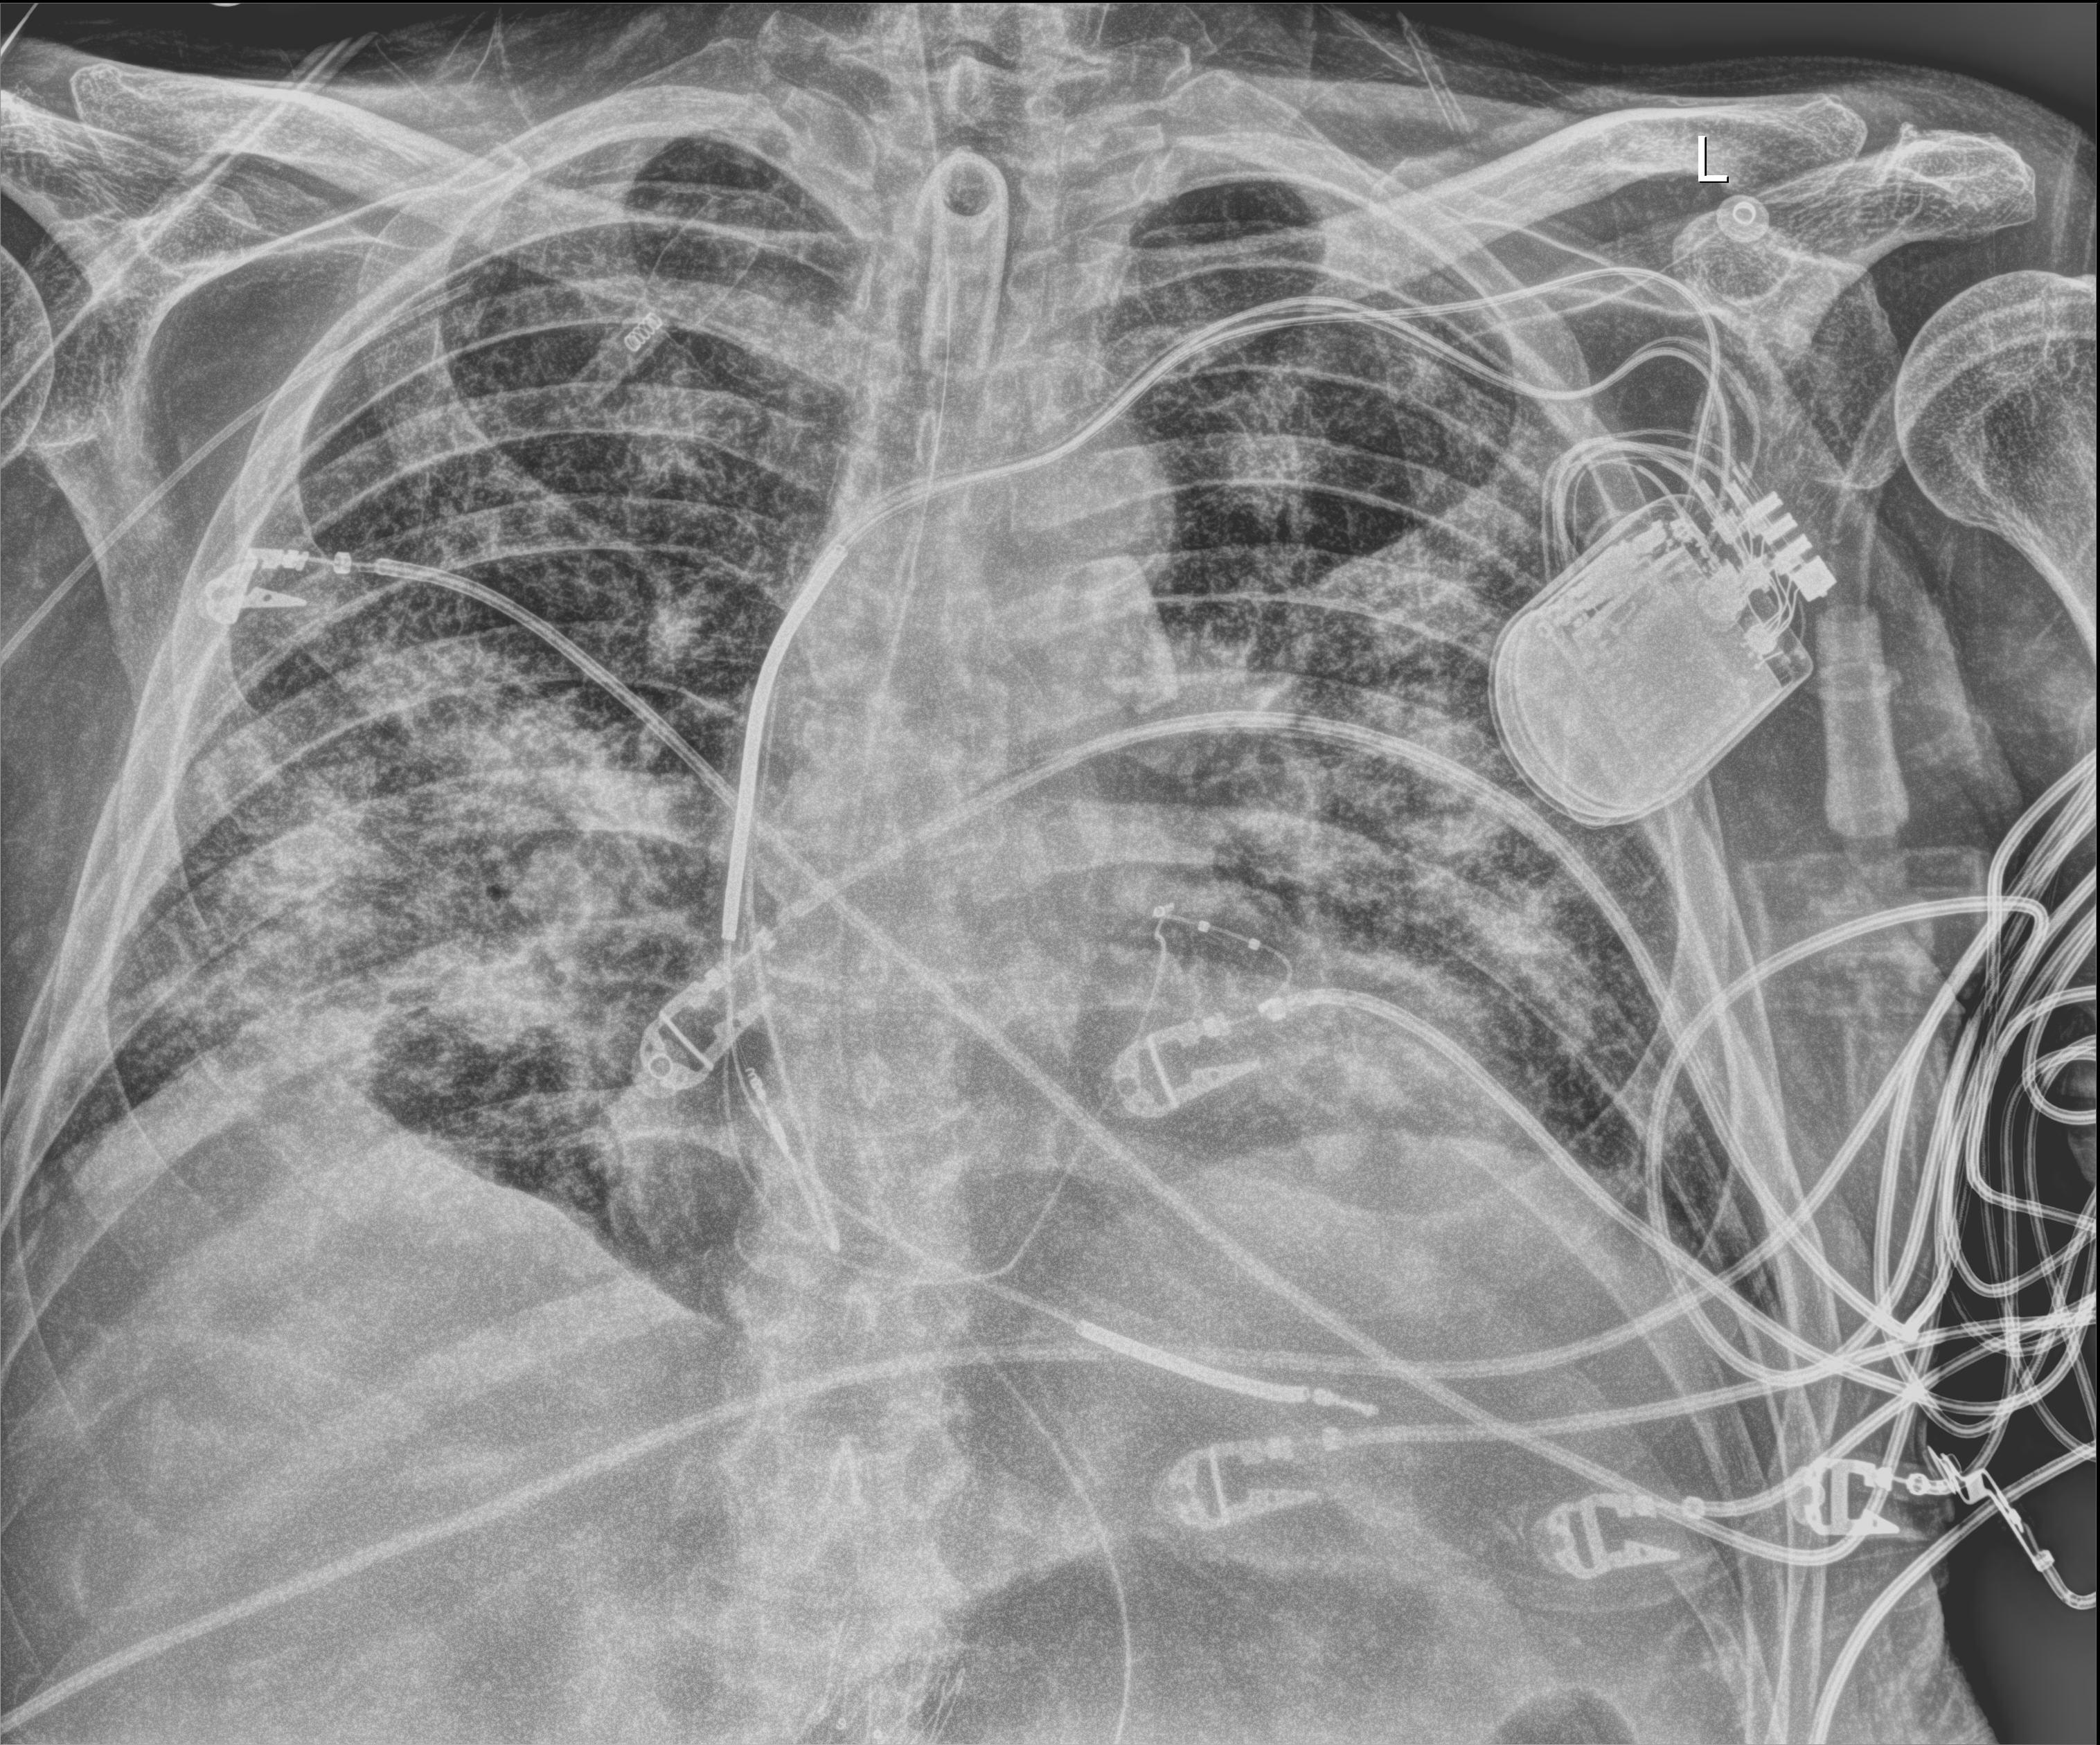
Portable chest radiograph, anteroposterior (AP) projection. Patient hospitalised with COVID-19; male, aged 60–74 years.
Admission-level facts for this patient (not findings on this image; timing relative to this image not recorded): admitted to intensive care during this hospital stay: yes.